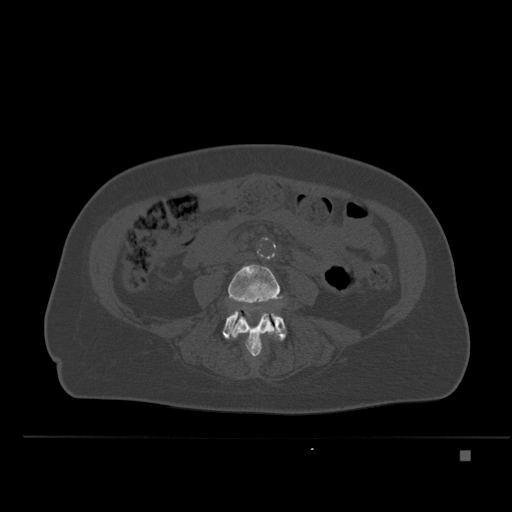
CT including the spine, one axial slice. Position 173 of 477 along the scan axis. Bone window (W 1800 / L 400 HU). 1.5 mm slice thickness. 512 × 512 image matrix, field of view 422 × 422 mm. Patient: female, 74 years. Case-level facts recorded for this patient, not image findings: primary cancer: colon.
Structures marked on this image (semi-automatically segmented with operator editing):
- L4 vertebra: bounding box <228,264,280,357> (left, top, right, bottom; pixels)
- L5 vertebra: <222,308,287,341>